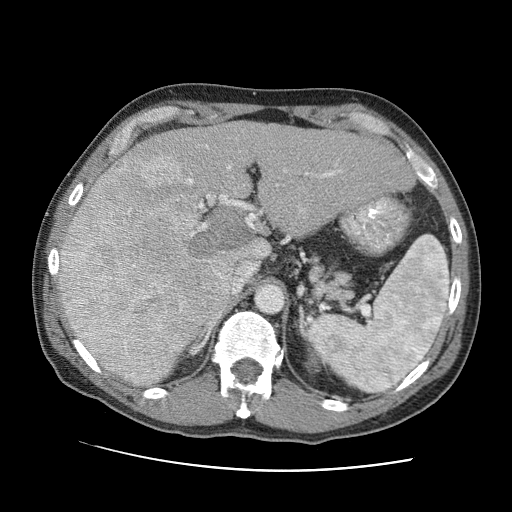
Contrast-enhanced abdominal CT (liver protocol), one axial slice. Slice 55 of 95 in the series (ordered by position). 120 kVp. One of 2 acquisitions stored at this slice position. Soft-tissue window (W 400 / L 40 HU). 2.5 mm slice thickness. 512 × 512 image matrix. From the clinical record (not read from this slice): diagnosis: hepatocellular carcinoma (patient treated with transarterial chemoembolisation; whether this scan precedes or follows treatment is not stated here); TNM stage (as recorded): Stage-IVA; Child-Pugh class: A; tumour differentiation: moderately differentiated.
Outlined on this slice (semi-automatic segmentation, software-assisted and operator-edited):
- abdominal aorta: bounding box (x1, y1, x2, y2) in pixels: (256, 285, 283, 312)
- liver parenchyma outside the tumour (the mass and vessels are separate outlines, so this box may not span the whole liver): (59, 121, 414, 386)
- mass: (56, 150, 254, 384)
- liver vessels: (198, 145, 340, 317)